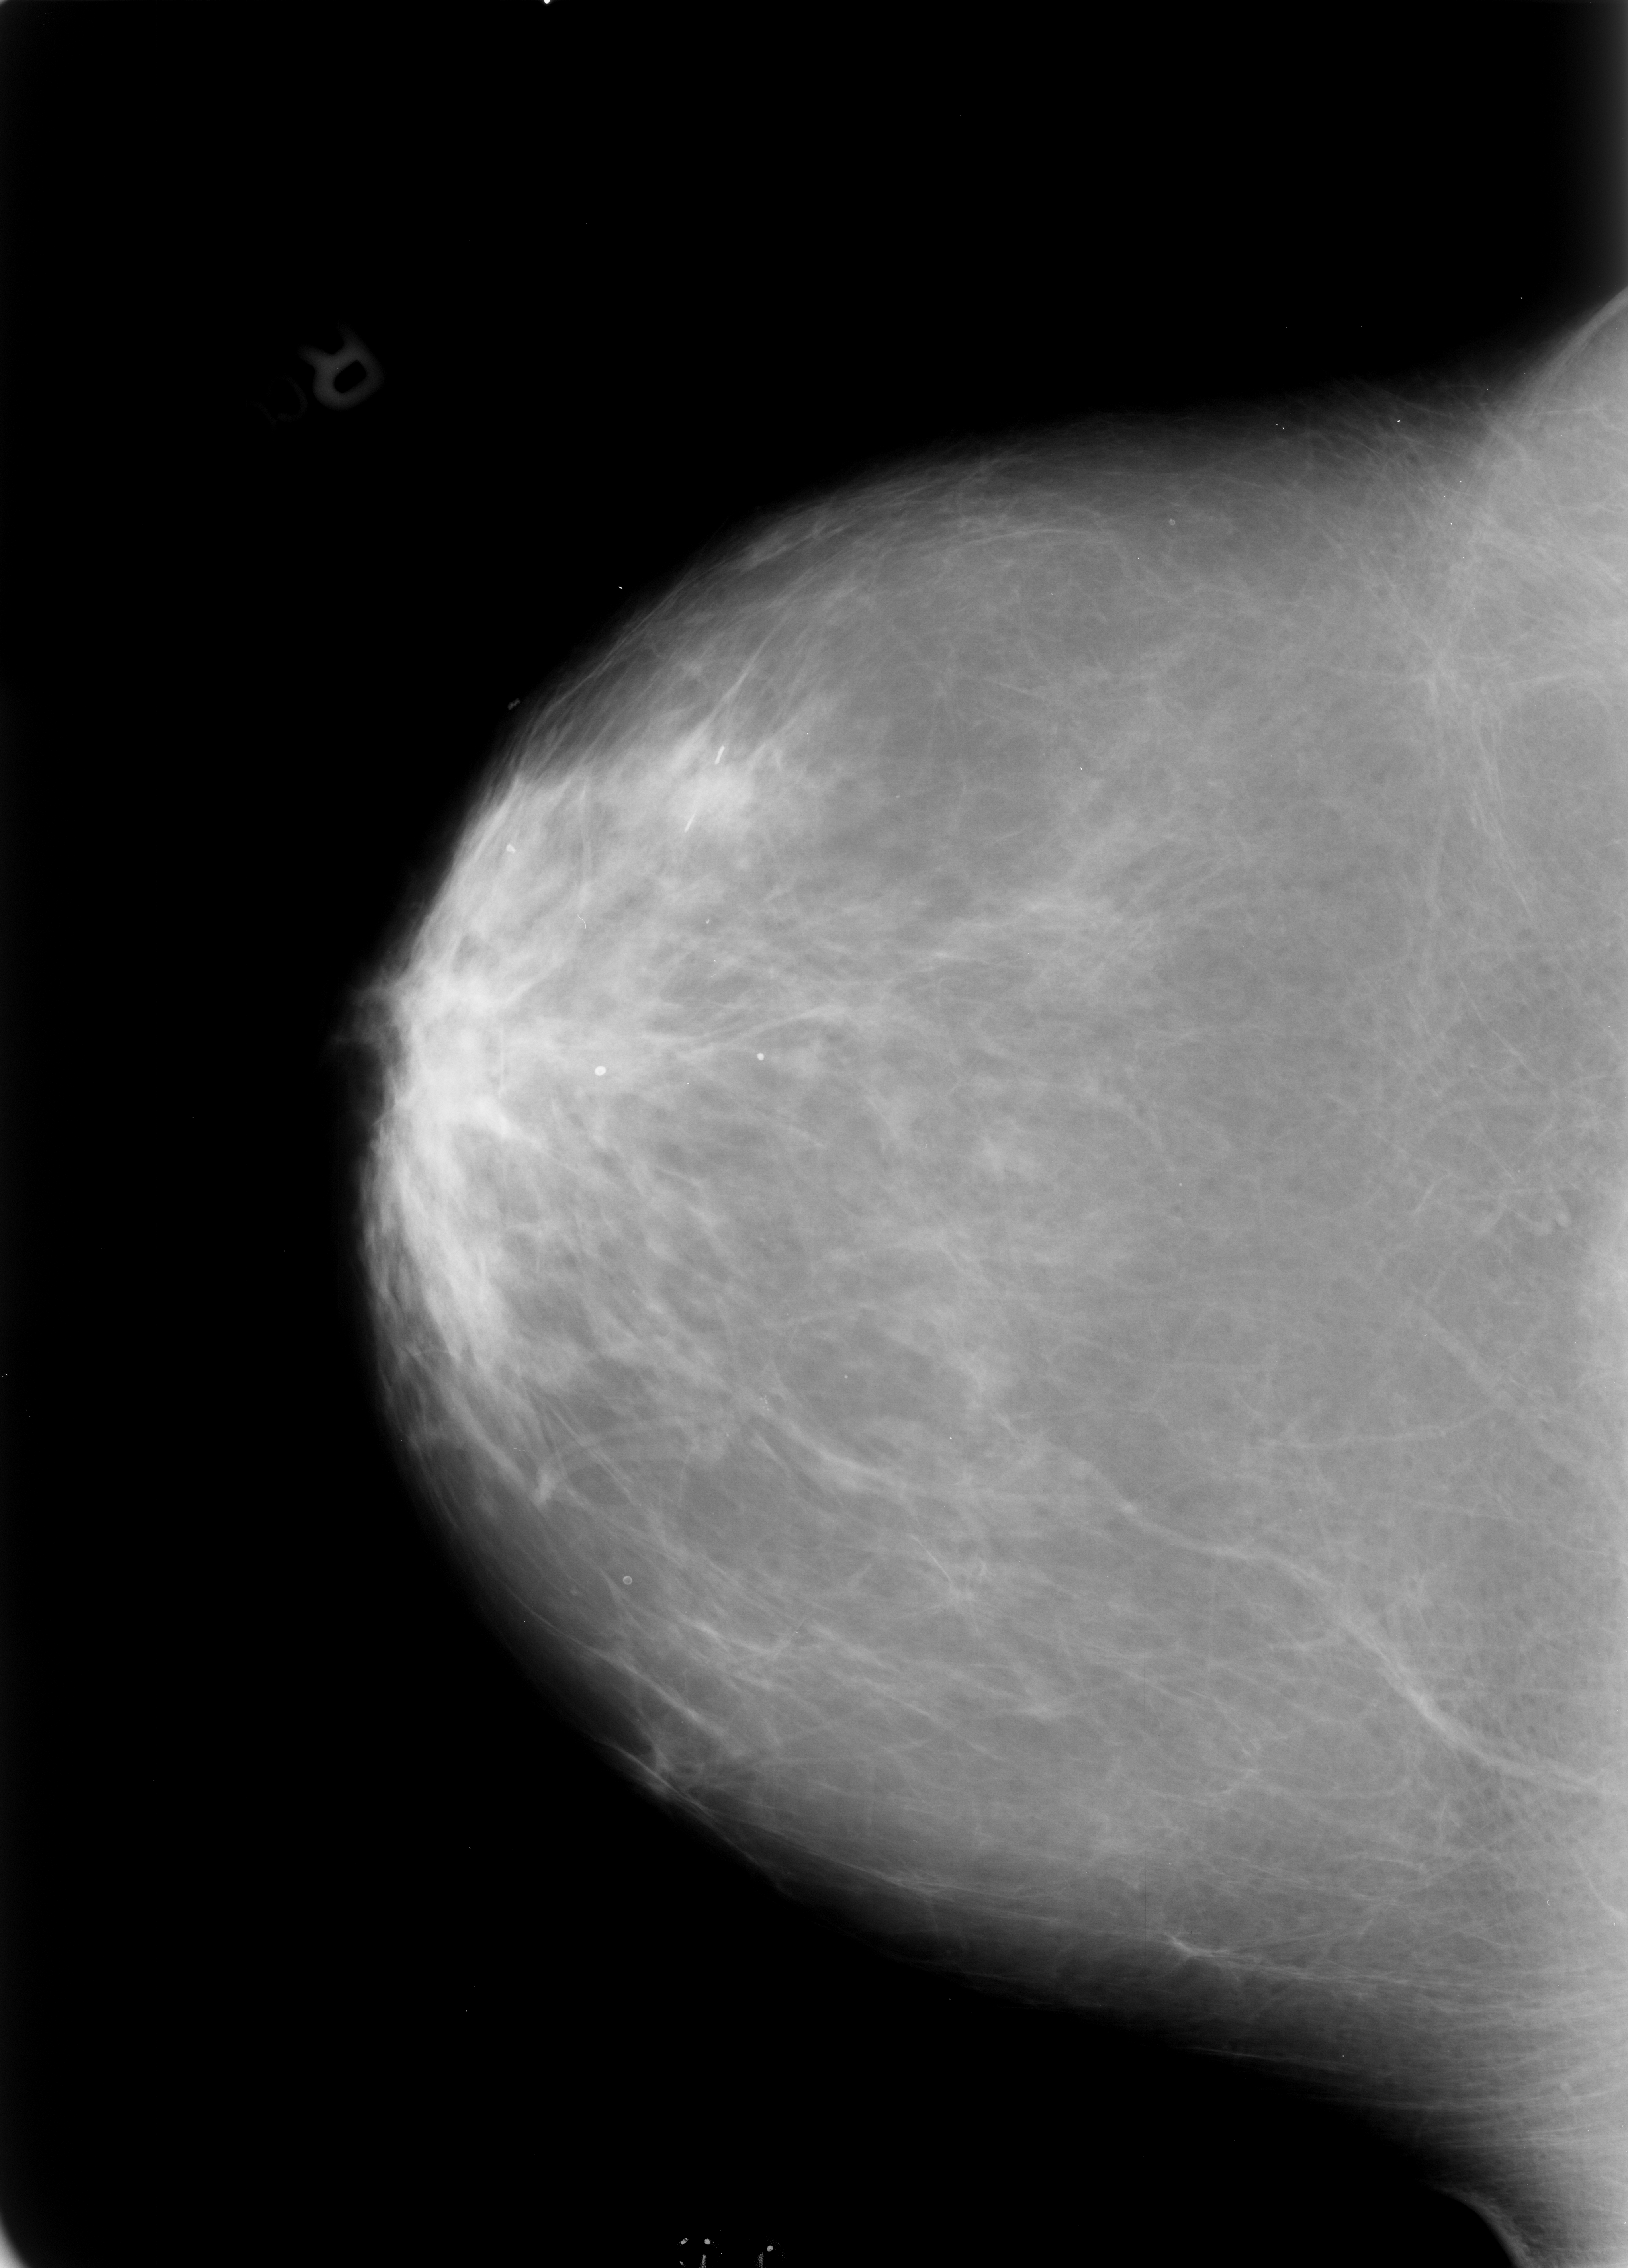
Mammogram (digitized film); right breast; craniocaudal (CC) view; breast composition: scattered fibroglandular densities (BI-RADS density category 2 of 4).
Calcifications, morphology pleomorphic, distribution clustered; BI-RADS assessment category 4; pathology result (as recorded, not read from the image): benign.